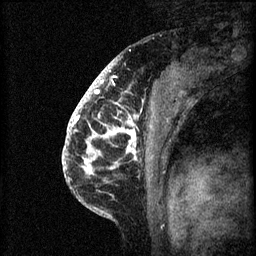
Breast MRI (dynamic contrast-enhanced), one sagittal slice. Slice 43 of 60 in the series (ordered by position). 3 images stored at this slice position (order not interpretable as contrast timing). 1.5 T. TE 4.2 ms, TR 8.2 ms. 2 mm slice thickness. 256 × 256 image matrix. Patient: female, 41 years.
Annotated regions visible in this slice (semi-automatic segmentation, software-assisted and operator-edited):
- analysis volume of interest (the breast-tissue region the enhancement analysis was run in; not a lesion): bounding box (x1, y1, x2, y2) in pixels: (72, 108, 155, 205)
- tumour enhancement mask (voxels above the 70 % enhancement threshold inside the analysis volume of interest): (72, 108, 137, 175)